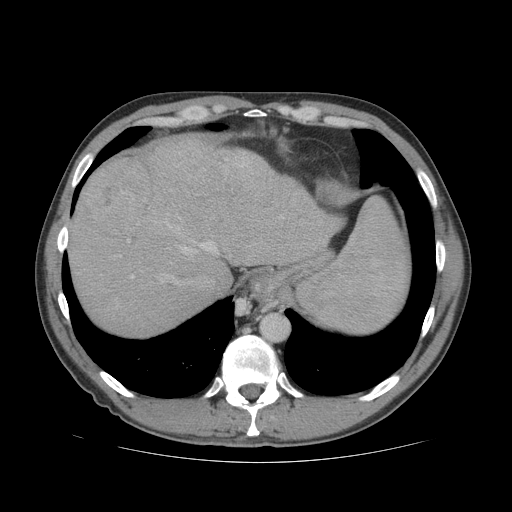
Contrast-enhanced abdominal CT (liver protocol), one axial slice; slice 61 of 81 in the series (ordered by position); reconstruction kernel STANDARD; 140 kVp; soft-tissue window (W 400 / L 40 HU); 2.5 mm slice thickness; 512 × 512 image matrix, field of view 400 × 400 mm. From the clinical record (not read from this slice): diagnosis: hepatocellular carcinoma (patient treated with transarterial chemoembolisation; whether this scan precedes or follows treatment is not stated here); TNM stage (as recorded): Stage-IVB; Child-Pugh class: B; tumour differentiation: well differentiated.
Structures marked on this image (semi-automatic segmentation, software-assisted and operator-edited):
- abdominal aorta: bounding box [x1, y1, x2, y2] px = [262, 314, 288, 339]
- liver parenchyma outside the tumour (the mass and vessels are separate outlines, so this box may not span the whole liver): [68, 136, 342, 336]
- mass: [82, 158, 152, 237]
- liver vessels: [131, 158, 283, 283]